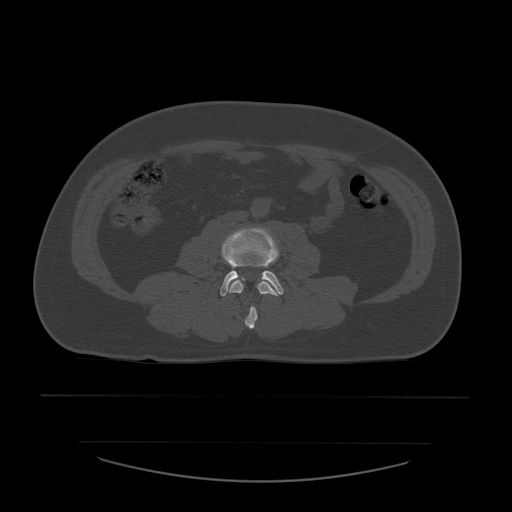
CT including the spine, one axial slice. Reconstruction kernel STANDARD. 120 kVp. Bone window (W 1800 / L 400 HU). 1.25 mm slice thickness. 512 × 512 image matrix, field of view 441 × 441 mm. Patient age 44 years. From the clinical record (not read from this slice): primary cancer: soft tissue sarcoma.
Outlined on this slice (semi-automatic segmentation, software-assisted and operator-edited):
- L3 vertebra: box from (x=228, y=279) to (x=278, y=329) px
- L4 vertebra: (x=220, y=228)–(x=284, y=297)